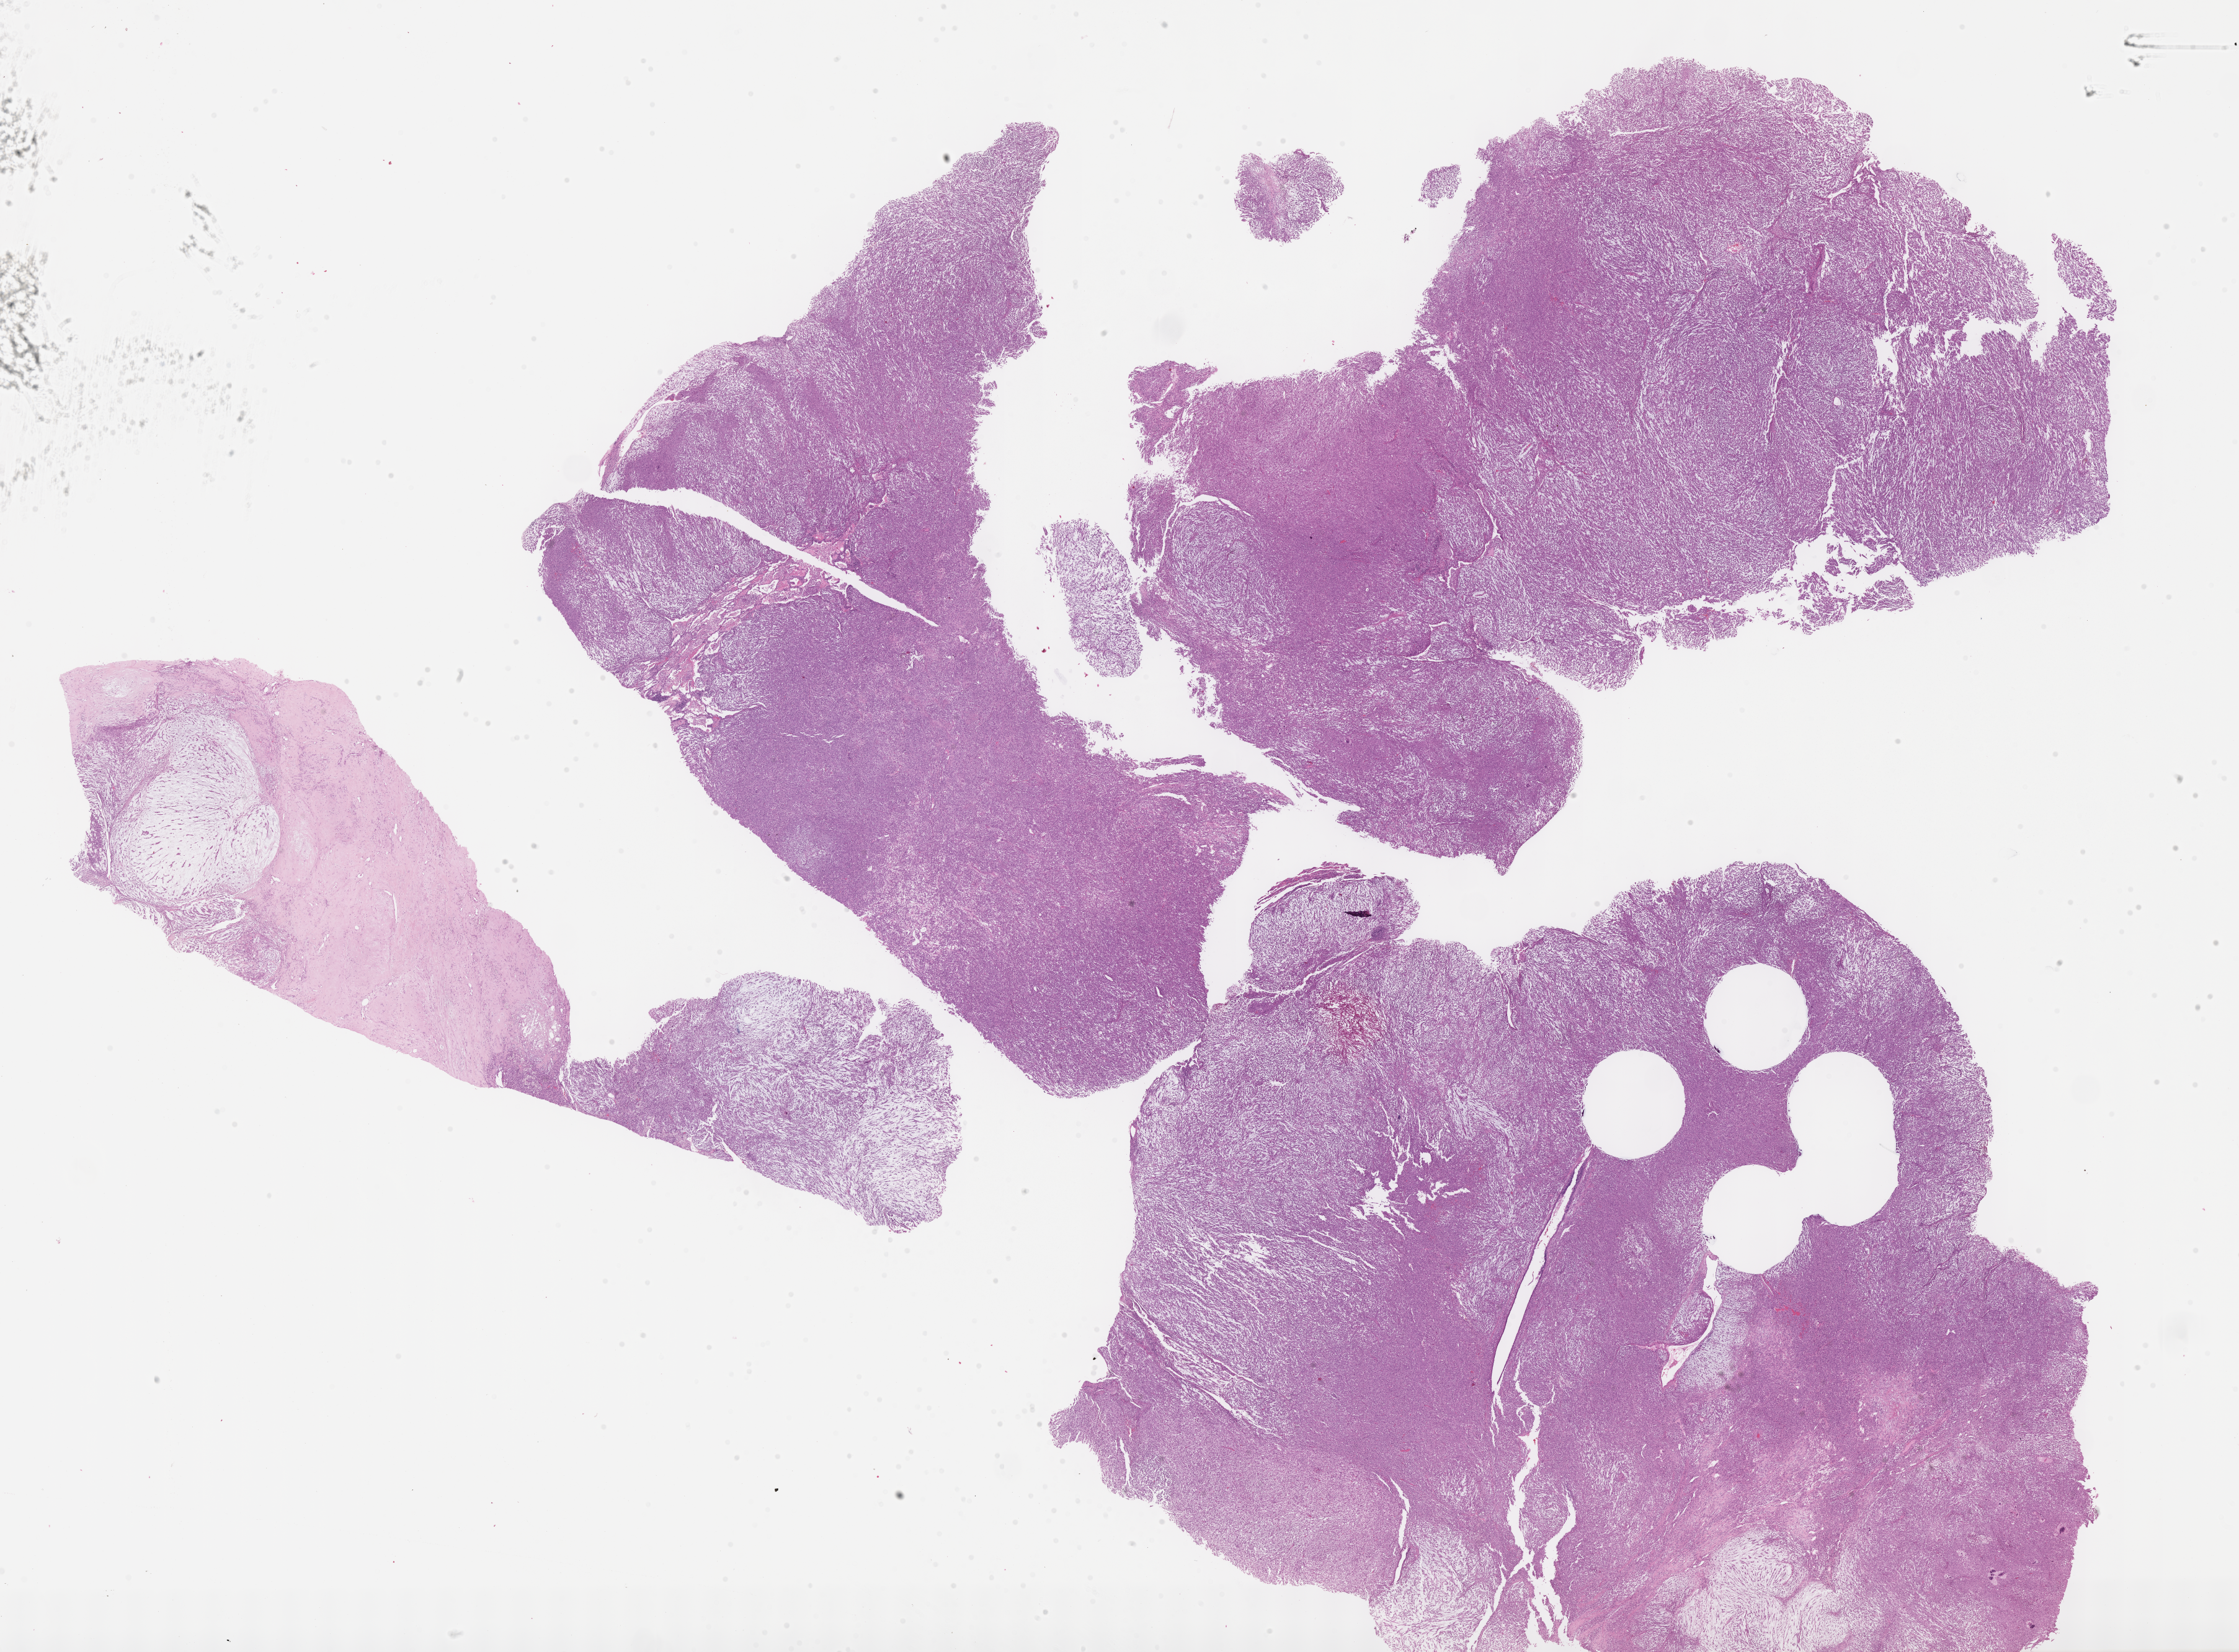
Whole-slide image, H&E stain of tumor tissue, whole scanned area (about 29.2 x 21.5 mm) shown as a low-resolution overview. Formalin-fixed paraffin-embedded section. Sample anatomic site: paratesticular, right. Patient: male, age 16.3 years at diagnosis.
• stage (as recorded): 1
• diagnosis: rhabdomyosarcoma; histological classification: embryonal rhabdomyosarcoma